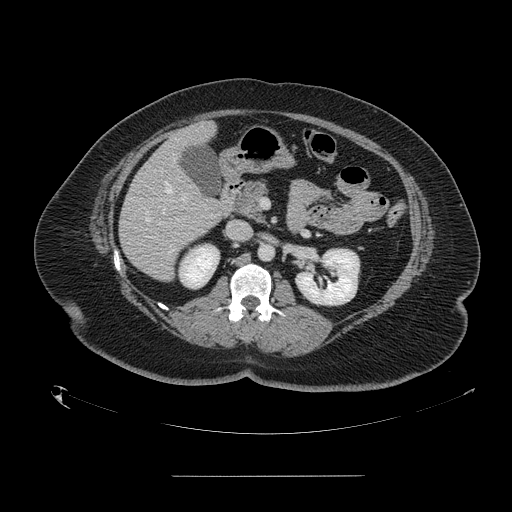
Contrast-enhanced abdominal CT, one axial slice; slice 71 of 164 in the series (ordered by position); soft-tissue window (W 400 / L 40 HU); 2.5 mm slice thickness; 512 × 512 image matrix, field of view 495 × 495 mm. Female patient, age 52 years. Case-level facts recorded for this patient, not image findings: diagnosis: colorectal cancer liver metastases, imaged before liver resection; multiple liver metastases: yes; largest metastasis: 3.5 cm; disease in both lobes: no.
Outlined on this slice (expert manual segmentation):
- hepatic veins: bounding box [x1, y1, x2, y2] px = [145, 182, 171, 221]
- liver: [120, 122, 231, 280]
- planned liver remnant (the part of the liver to remain after resection): [179, 122, 216, 148]
- portal vein (with intrahepatic branches): [181, 198, 185, 200]